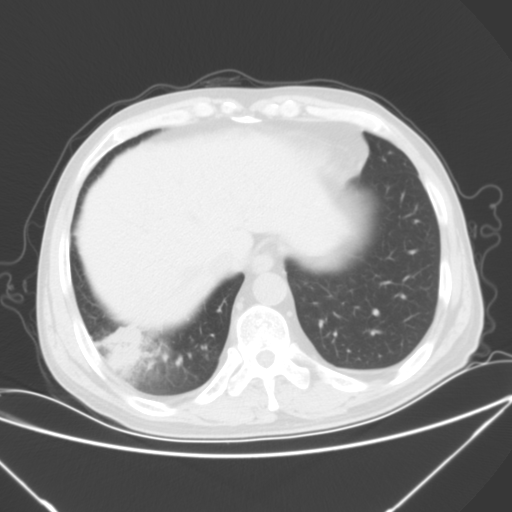
Chest CT, one axial slice; slice 16 of 57 in the series (ordered by position); 120 kVp; lung window (W 1500 / L -600 HU); 5 mm slice thickness; 512 × 512 image matrix, field of view 364 × 364 mm. Male patient, age 54 years. Case-level facts recorded for this patient, not image findings: clinical TNM (as recorded): T2 N1 M0.
Annotated regions visible in this slice (bounding box drawn by a radiologist):
- lung tumour (recorded histology: adenocarcinoma): bounding box (x1, y1, x2, y2) in pixels: (100, 321, 144, 371)